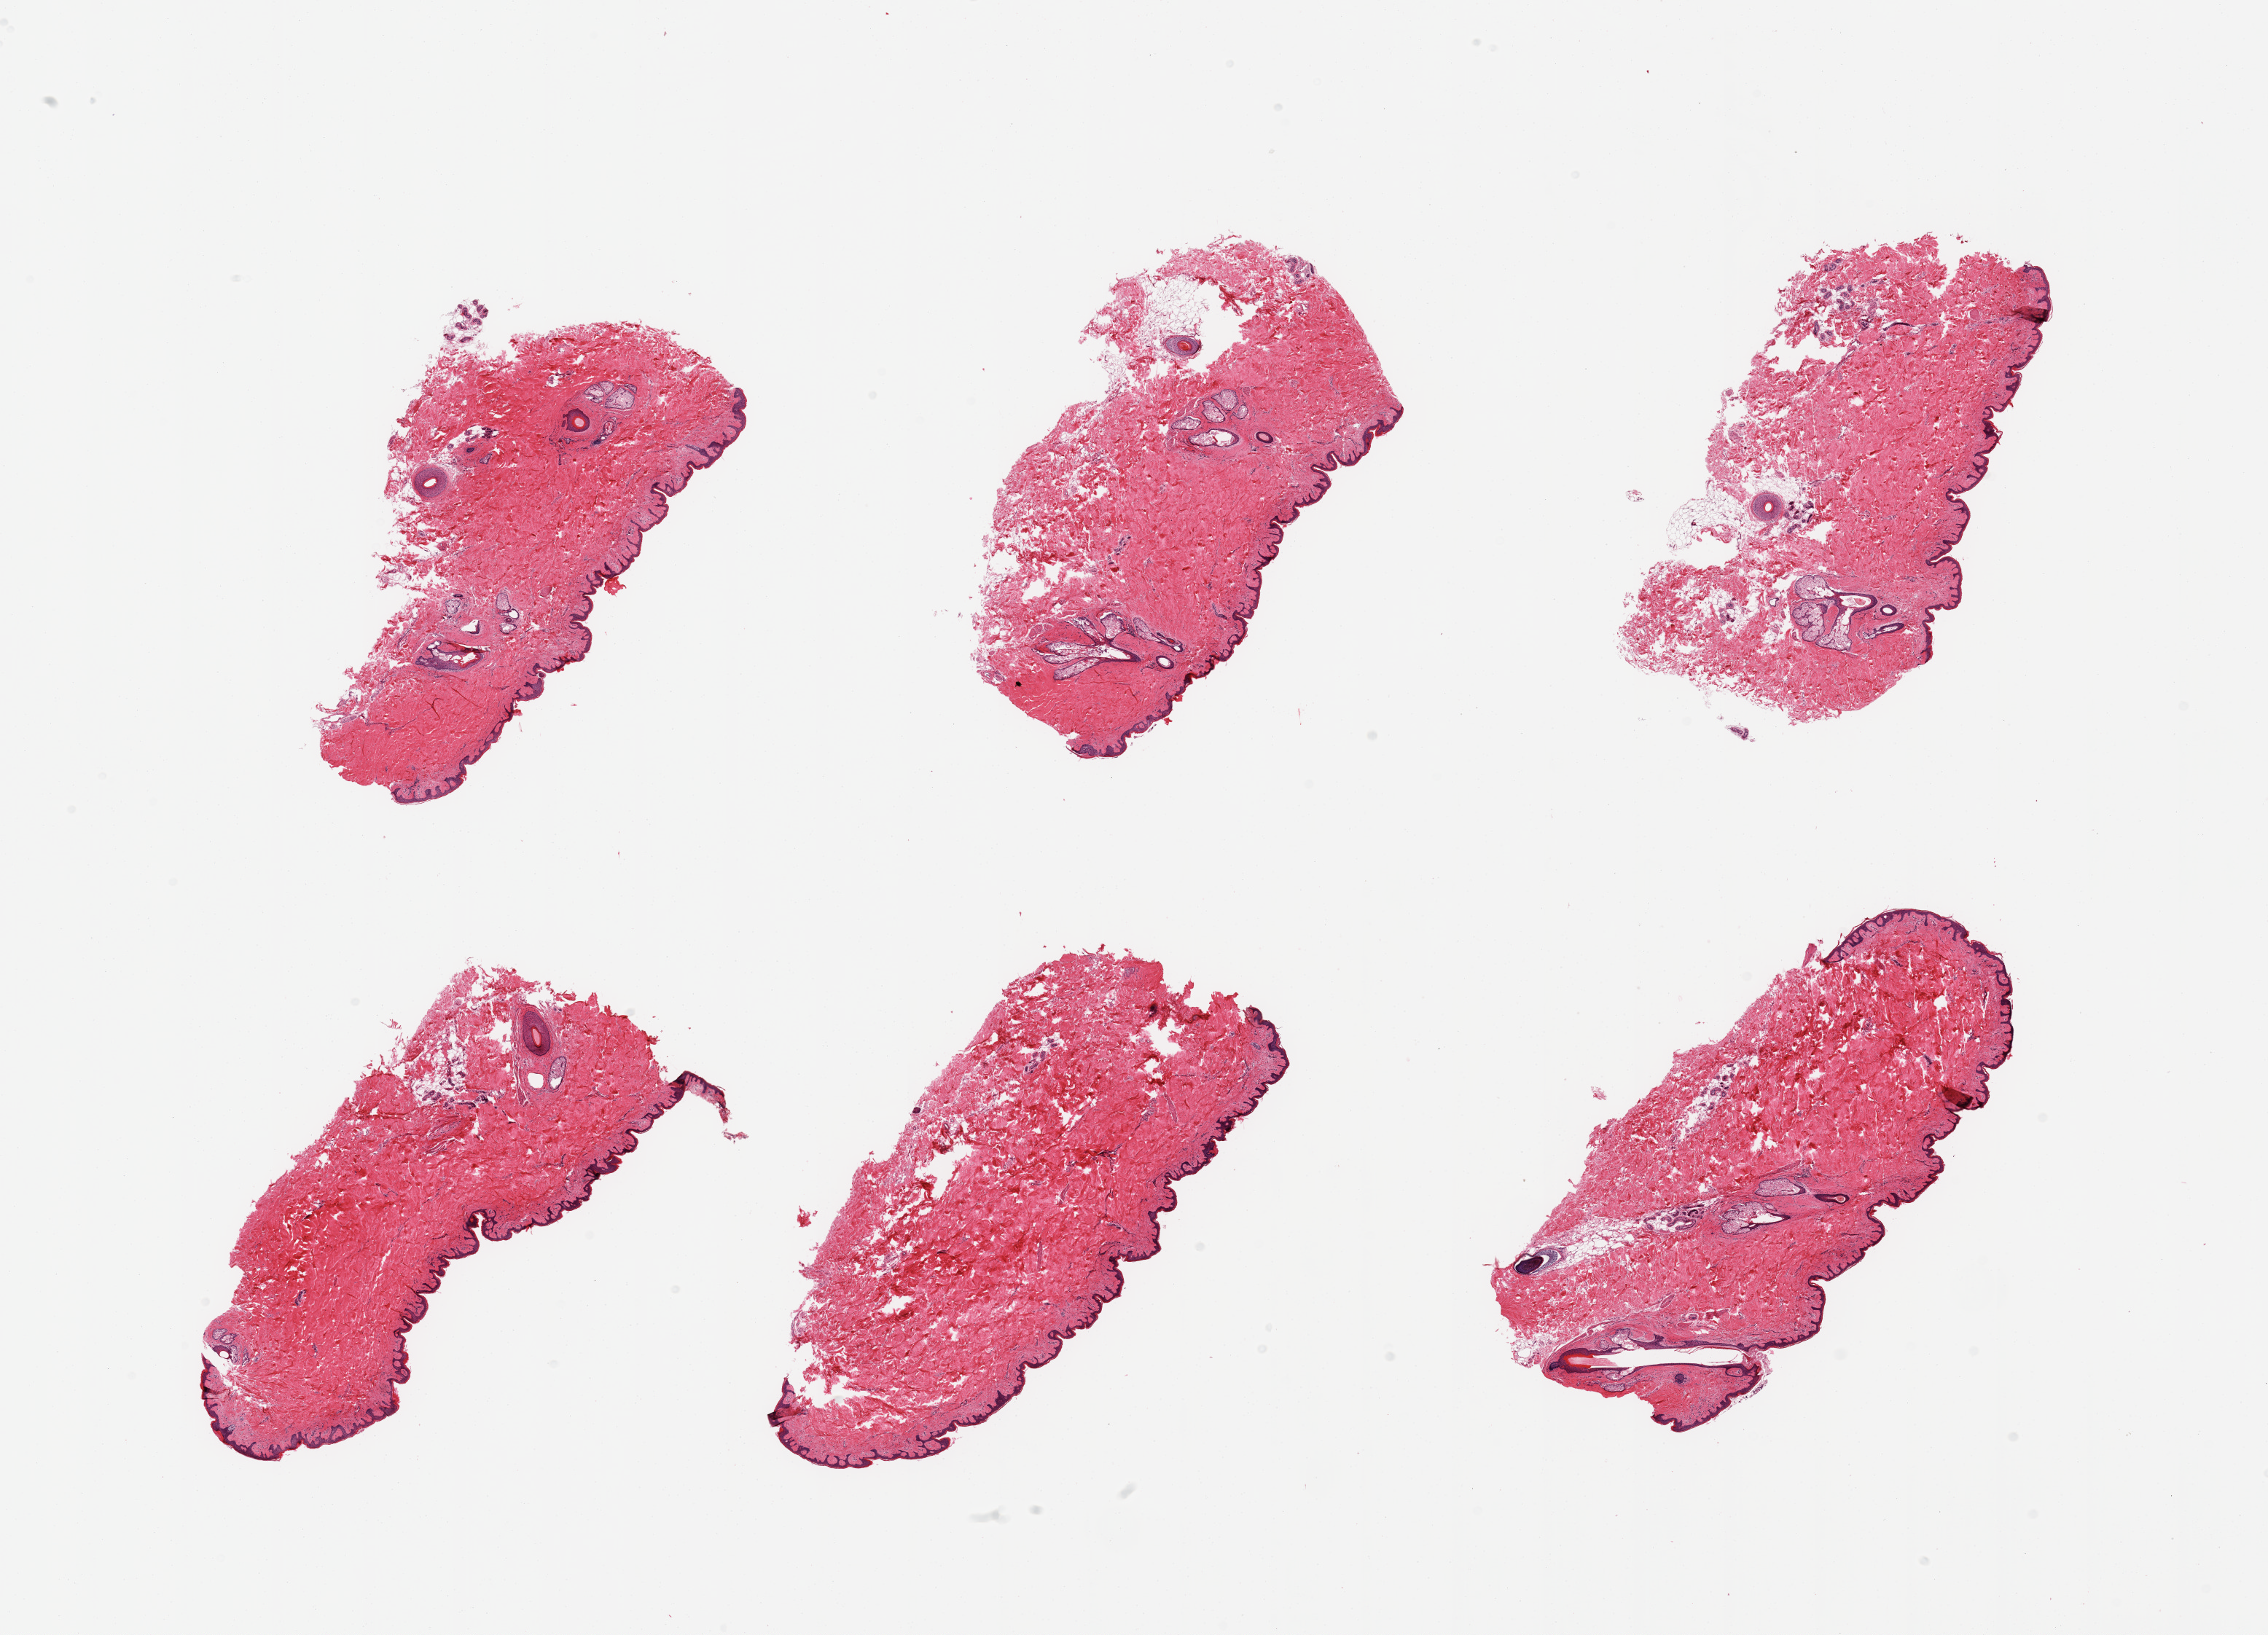
Whole-slide image, H&E stain — a low-resolution overview of the entire scanned area, about 24.6 x 17.7 mm. PAXgene-fixed paraffin-embedded (PFPE) section. Target tissue: skin of suprapubic region. Tissue donor sample. Donor: male.
• reviewer comment on this tissue sample: 6 pieces, squamous epithelium is ~30-40 microns; minimal dermal fat